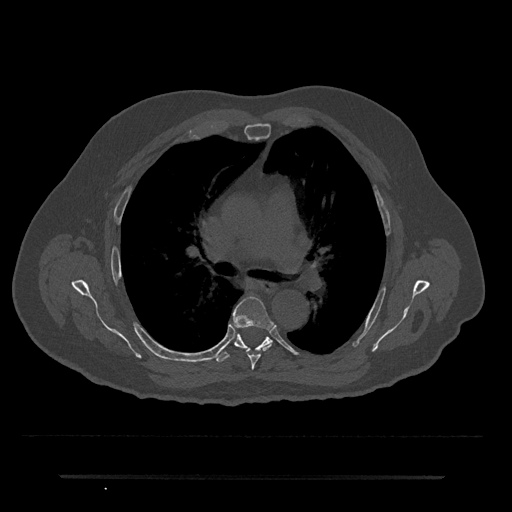
CT including the spine, one axial slice. Position 462 of 797 along the scan axis. Reconstruction kernel Br40s/3. 120 kVp. Bone window (W 1800 / L 400 HU). 0.5 mm slice thickness. 512 × 512 image matrix, field of view 437 × 437 mm. Patient: male, 69 years. From the clinical record (not read from this slice): primary cancer: prostate.
Annotated regions visible in this slice (semi-automatically segmented with operator editing):
- T5 vertebra: box from (x=233, y=296) to (x=274, y=370) px
- T6 vertebra: (x=216, y=321)–(x=272, y=363)